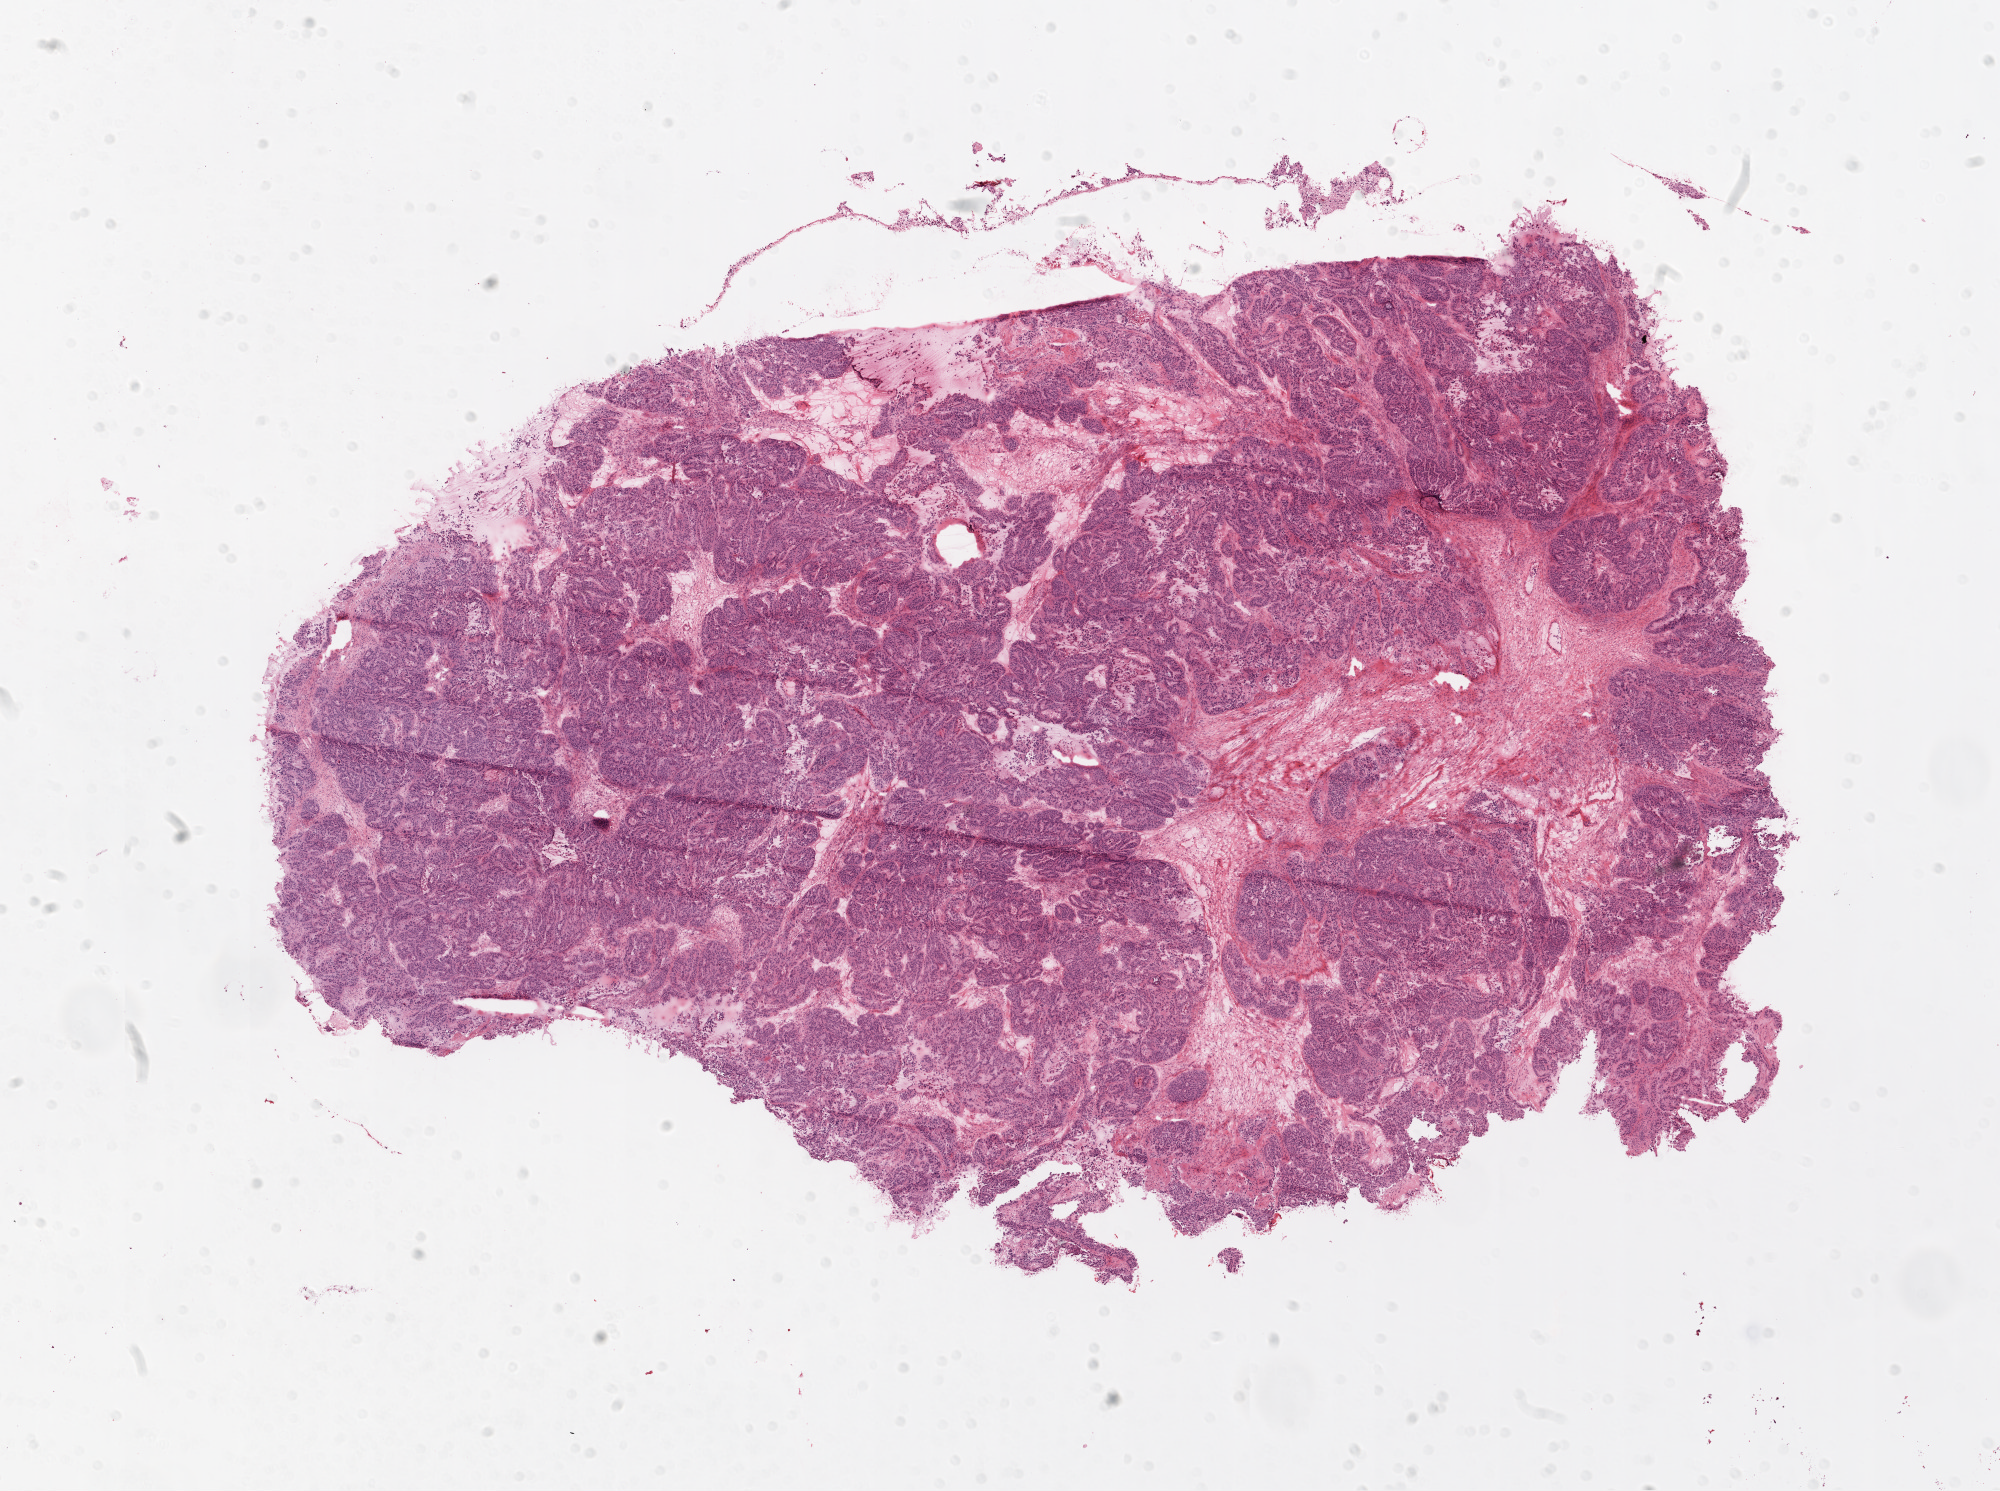
H&E whole-slide image, shown as a low-resolution overview of the whole scanned area (about 16.0 x 12.0 mm, acquisition: 20x scan), frozen section from the top of the tissue portion, ovary, primary tumour sample. Female, age 52 years at initial diagnosis. Histologic grade: G3 (poorly differentiated). Composition of this section per pathologist review: tumour cells 90%, tumour nuclei 99%, normal cells 0%, stromal cells 10%, necrosis 0%.
• laterality: bilateral
• pathologic diagnosis: Serous cystadenocarcinoma, NOS
• FIGO stage: IC